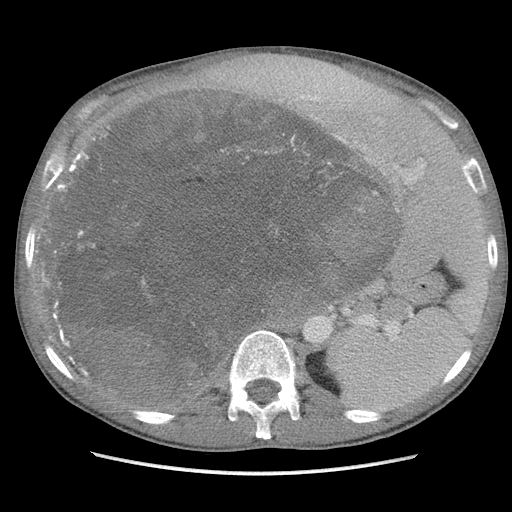
Contrast-enhanced abdominal CT, one axial slice. Slice 72 of 115 in the series (ordered by position). Soft-tissue window (W 400 / L 40 HU). 5 mm slice thickness. 512 × 512 image matrix, field of view 360 × 360 mm. Male patient. From the clinical record (not read from this slice): diagnosis: adrenocortical carcinoma; tumour side: right adrenal; Ki-67 index: 13 %; stage (as recorded): 3.
Annotated regions visible in this slice (semi-automatically segmented with operator editing):
- mass: bounding box <63,97,389,403> (left, top, right, bottom; pixels)